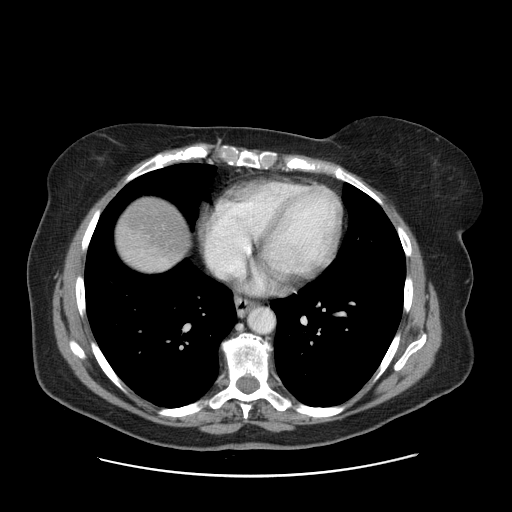
Contrast-enhanced abdominal CT, one axial slice; position 151 of 161 along the scan axis; 120 kVp; soft-tissue window (W 400 / L 40 HU); 2.5 mm slice thickness; 512 × 512 image matrix. Female patient, age 62 years. Case-level facts recorded for this patient, not image findings: diagnosis: colorectal cancer liver metastases, imaged before liver resection; multiple liver metastases: no; largest metastasis: 2.5 cm; disease in both lobes: no.
Structures marked on this image (manually delineated by an expert):
- liver: bounding box <117,199,188,270> (left, top, right, bottom; pixels)
- planned liver remnant (the part of the liver to remain after resection): <117,199,187,266>